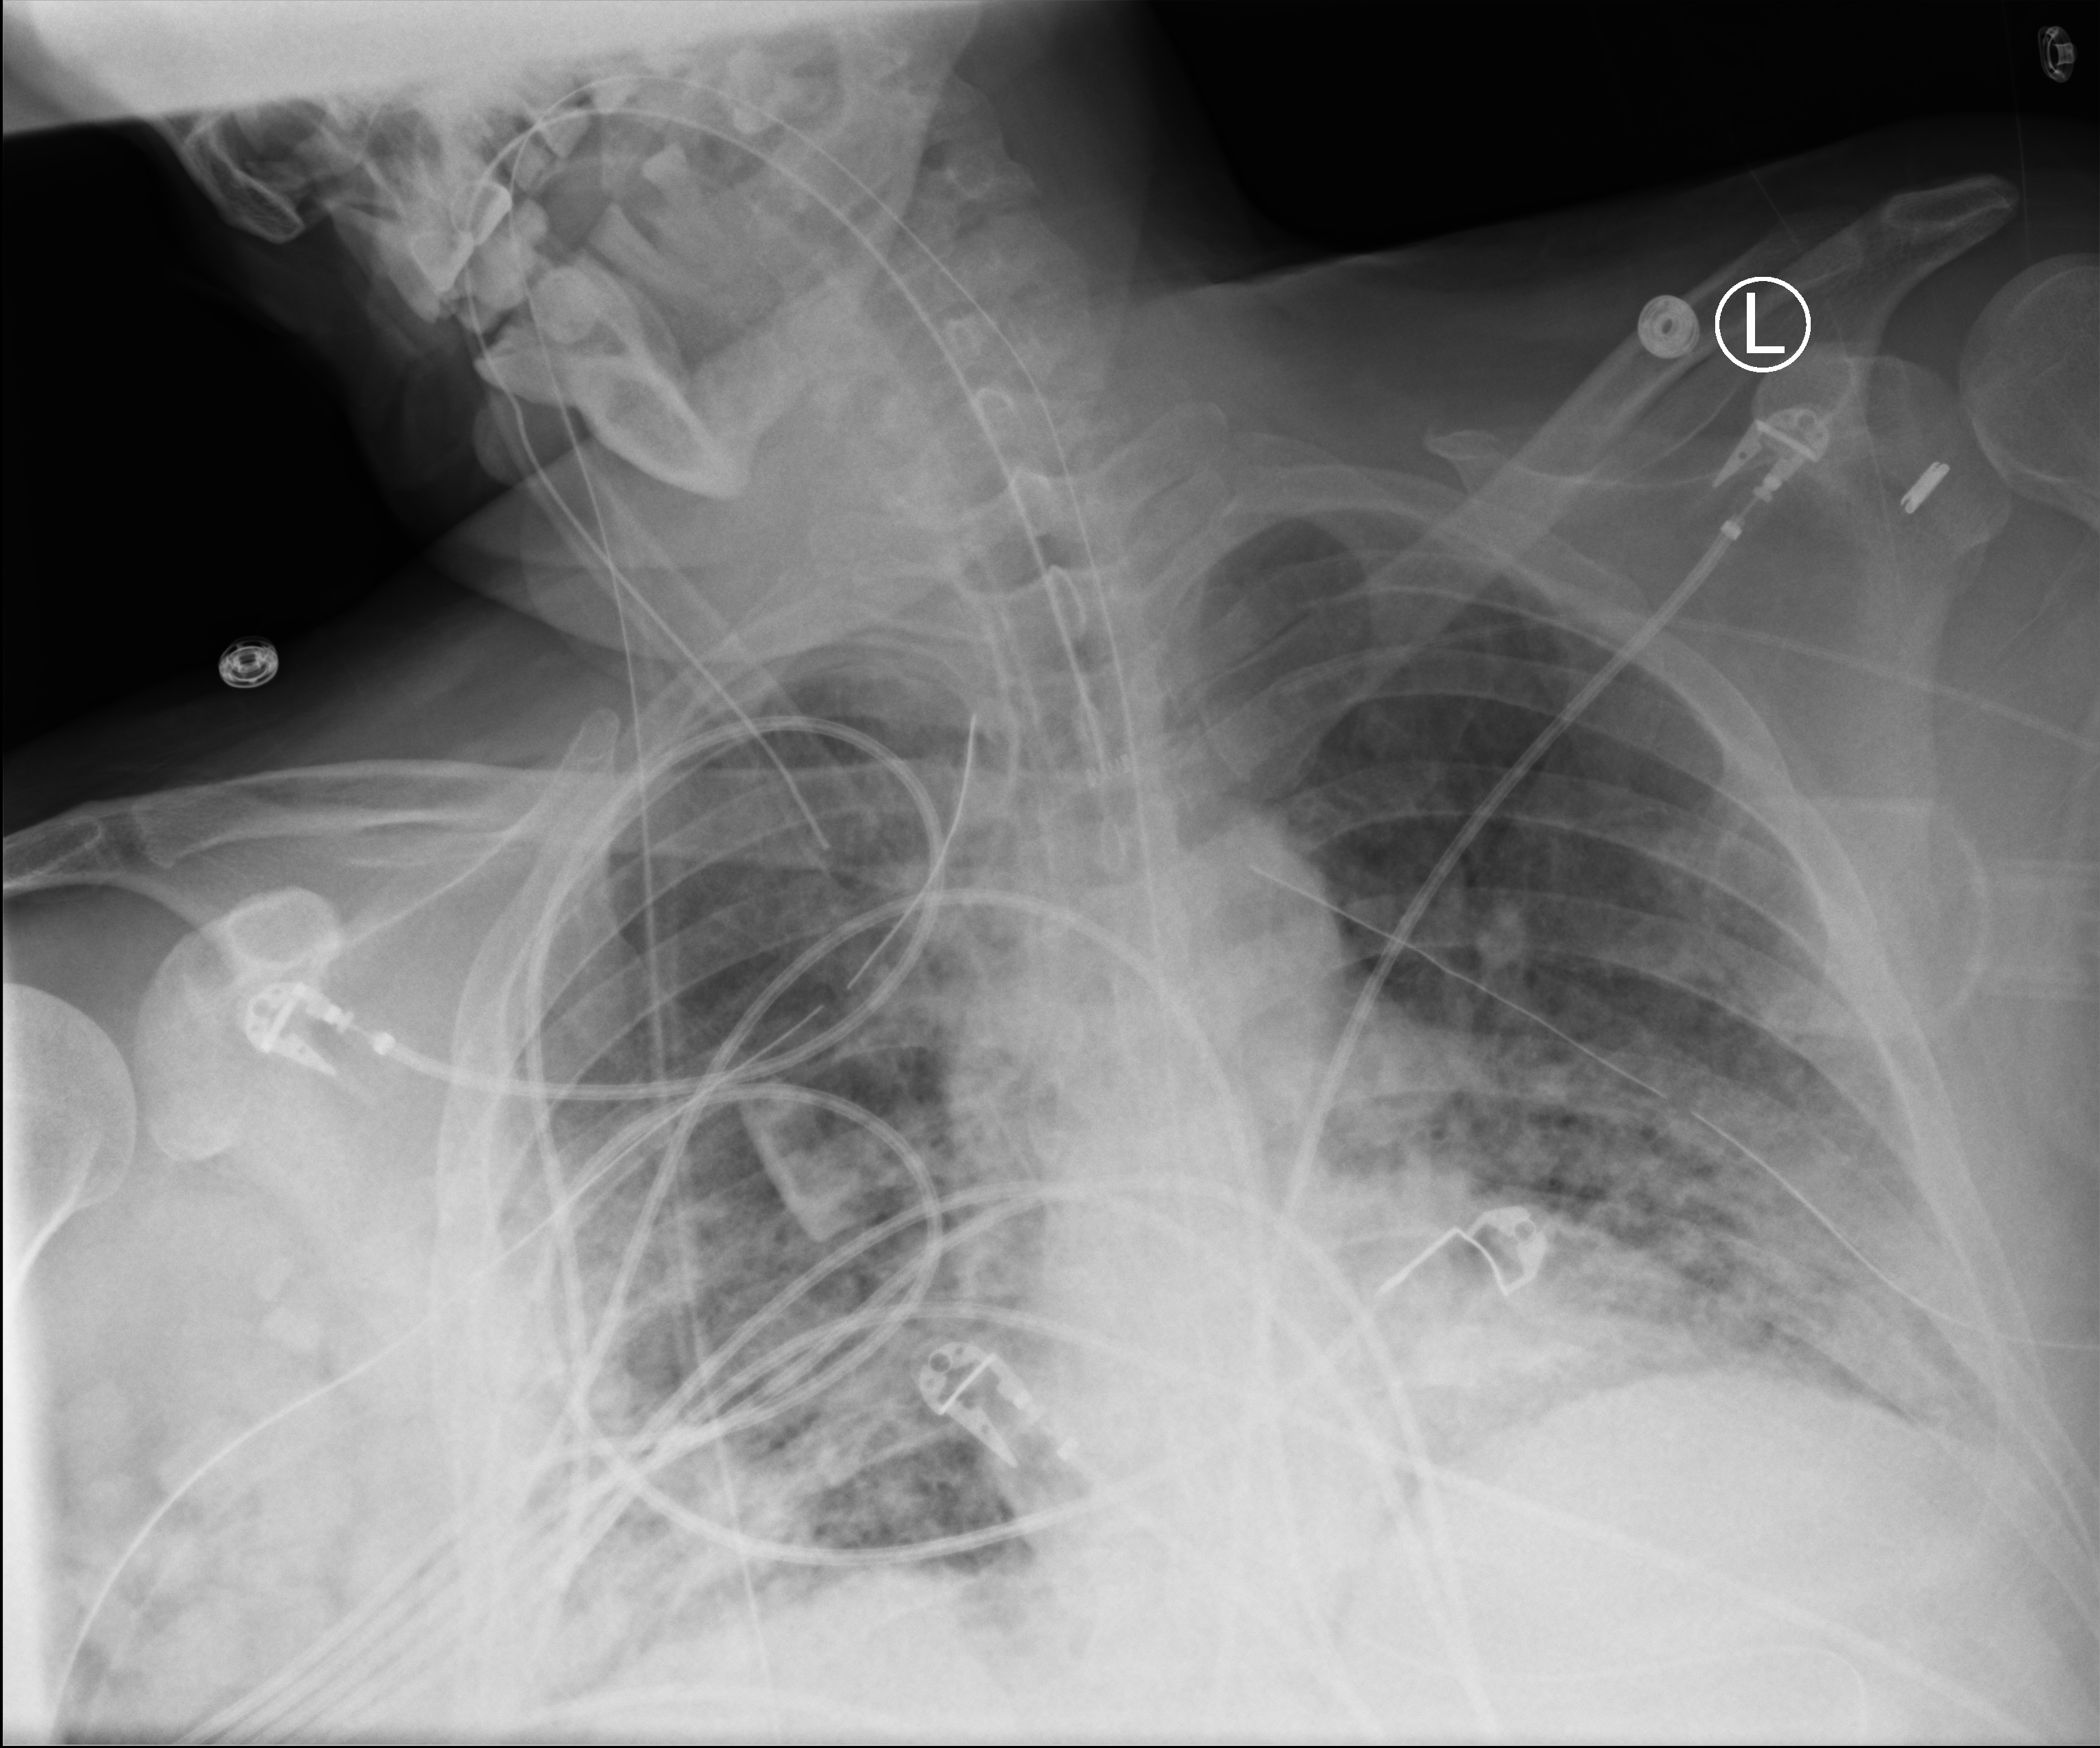
Portable chest radiograph; anteroposterior (AP) projection. Patient hospitalised with COVID-19; male, aged 18–59 years.
Admission-level facts for this patient (not findings on this image; timing relative to this image not recorded): chronic kidney disease (admission record): no; admitted to intensive care during this hospital stay: yes; length of hospital stay: 63 days.